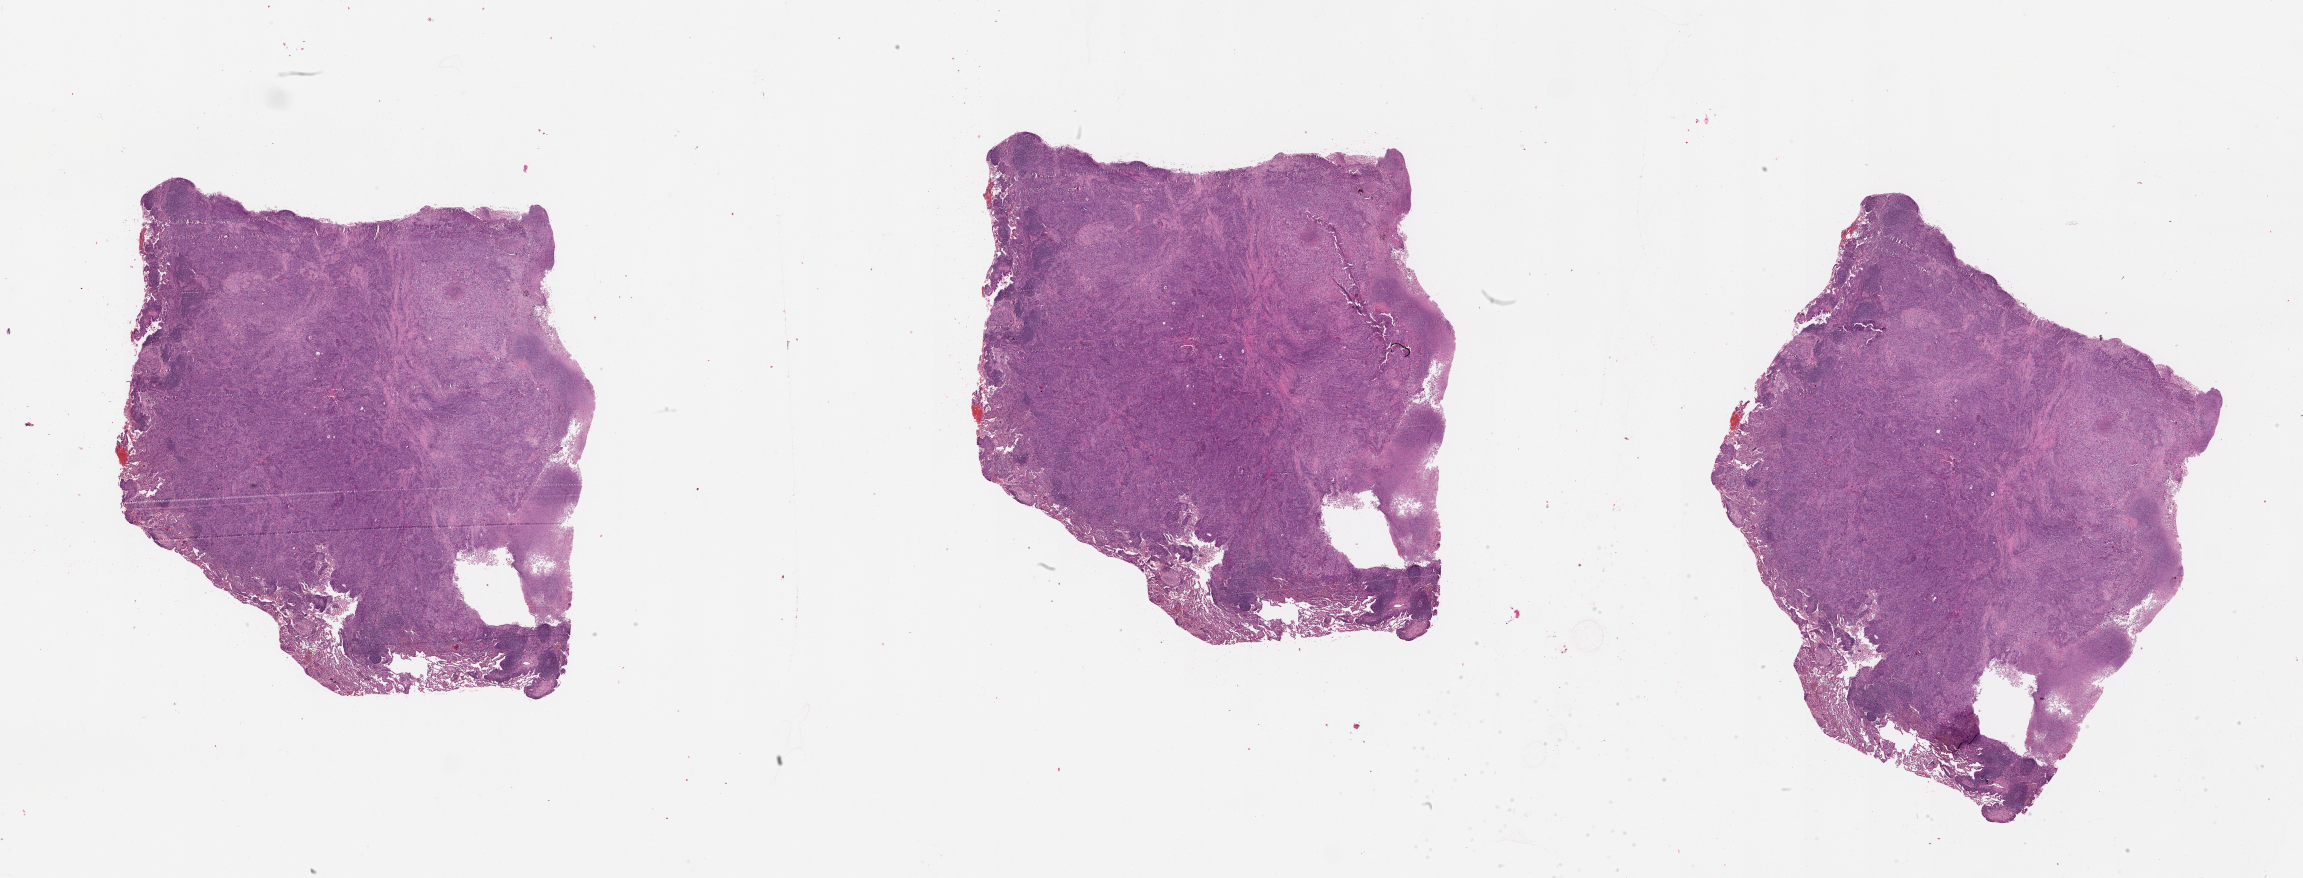
H&E-stained whole-slide image, whole scanned area (about 37.1 x 14.1 mm, from a 20x scan) shown as a low-resolution overview. Tumour tissue sample, lung. Male, 77 y/o.
* patient diagnosis (cohort enrolment): squamous cell carcinoma (lung)